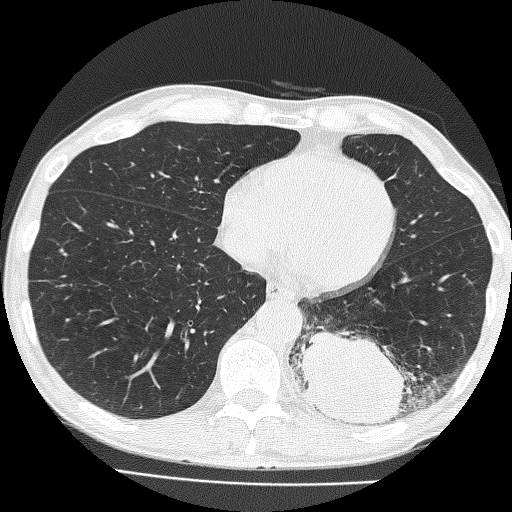
Chest CT (low-dose screening protocol), one axial image; baseline screening round; lung window (W 1500 / L -600 HU); 2 mm slice thickness; lung (sharp) reconstruction kernel (FC51); slice 104 of 160 in the series; 512 × 512 image matrix. Male, age 58 years at enrolment.
Expert reader's lesion annotation, bounding box (x1, y1, x2, y2) in pixels: (293, 298, 428, 435). The screening reader recorded 2 non-calcified nodules or masses ≥4 mm on this exam; which of them this box marks is not recorded.